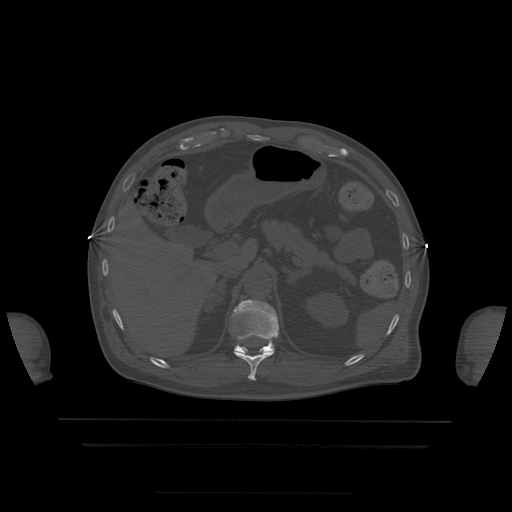
CT including the spine, one axial slice; bone window (W 1800 / L 400 HU); 1.25 mm slice thickness; 512 × 512 image matrix, field of view 436 × 436 mm. Patient age 68 years. Case-level facts recorded for this patient, not image findings: primary cancer: urothelial.
Annotated regions visible in this slice (semi-automatically segmented with operator editing):
- T11 vertebra: bounding box (x1, y1, x2, y2) in pixels: (234, 350, 274, 381)
- T12 vertebra: (231, 300, 279, 353)